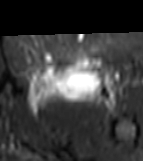
MRI of an extremity soft-tissue mass, one axial slice; position 42 of 81 along the scan axis; STIR; MR volume resampled by the dataset authors to the PET/CT grid (not the native acquisition matrix); 143 × 161 image matrix. Female patient. From the clinical record (not read from this slice): histological type: myxofibrosarcoma; grade: intermediate; site of the primary tumour: left thigh.
Outlined on this slice (expert contour drawn on MRI and transferred to this co-registered scan by the dataset authors):
- gross tumour volume including surrounding oedema: box from (x=24, y=58) to (x=119, y=111) px
- gross tumour volume (mass): (x=40, y=58)–(x=98, y=96)